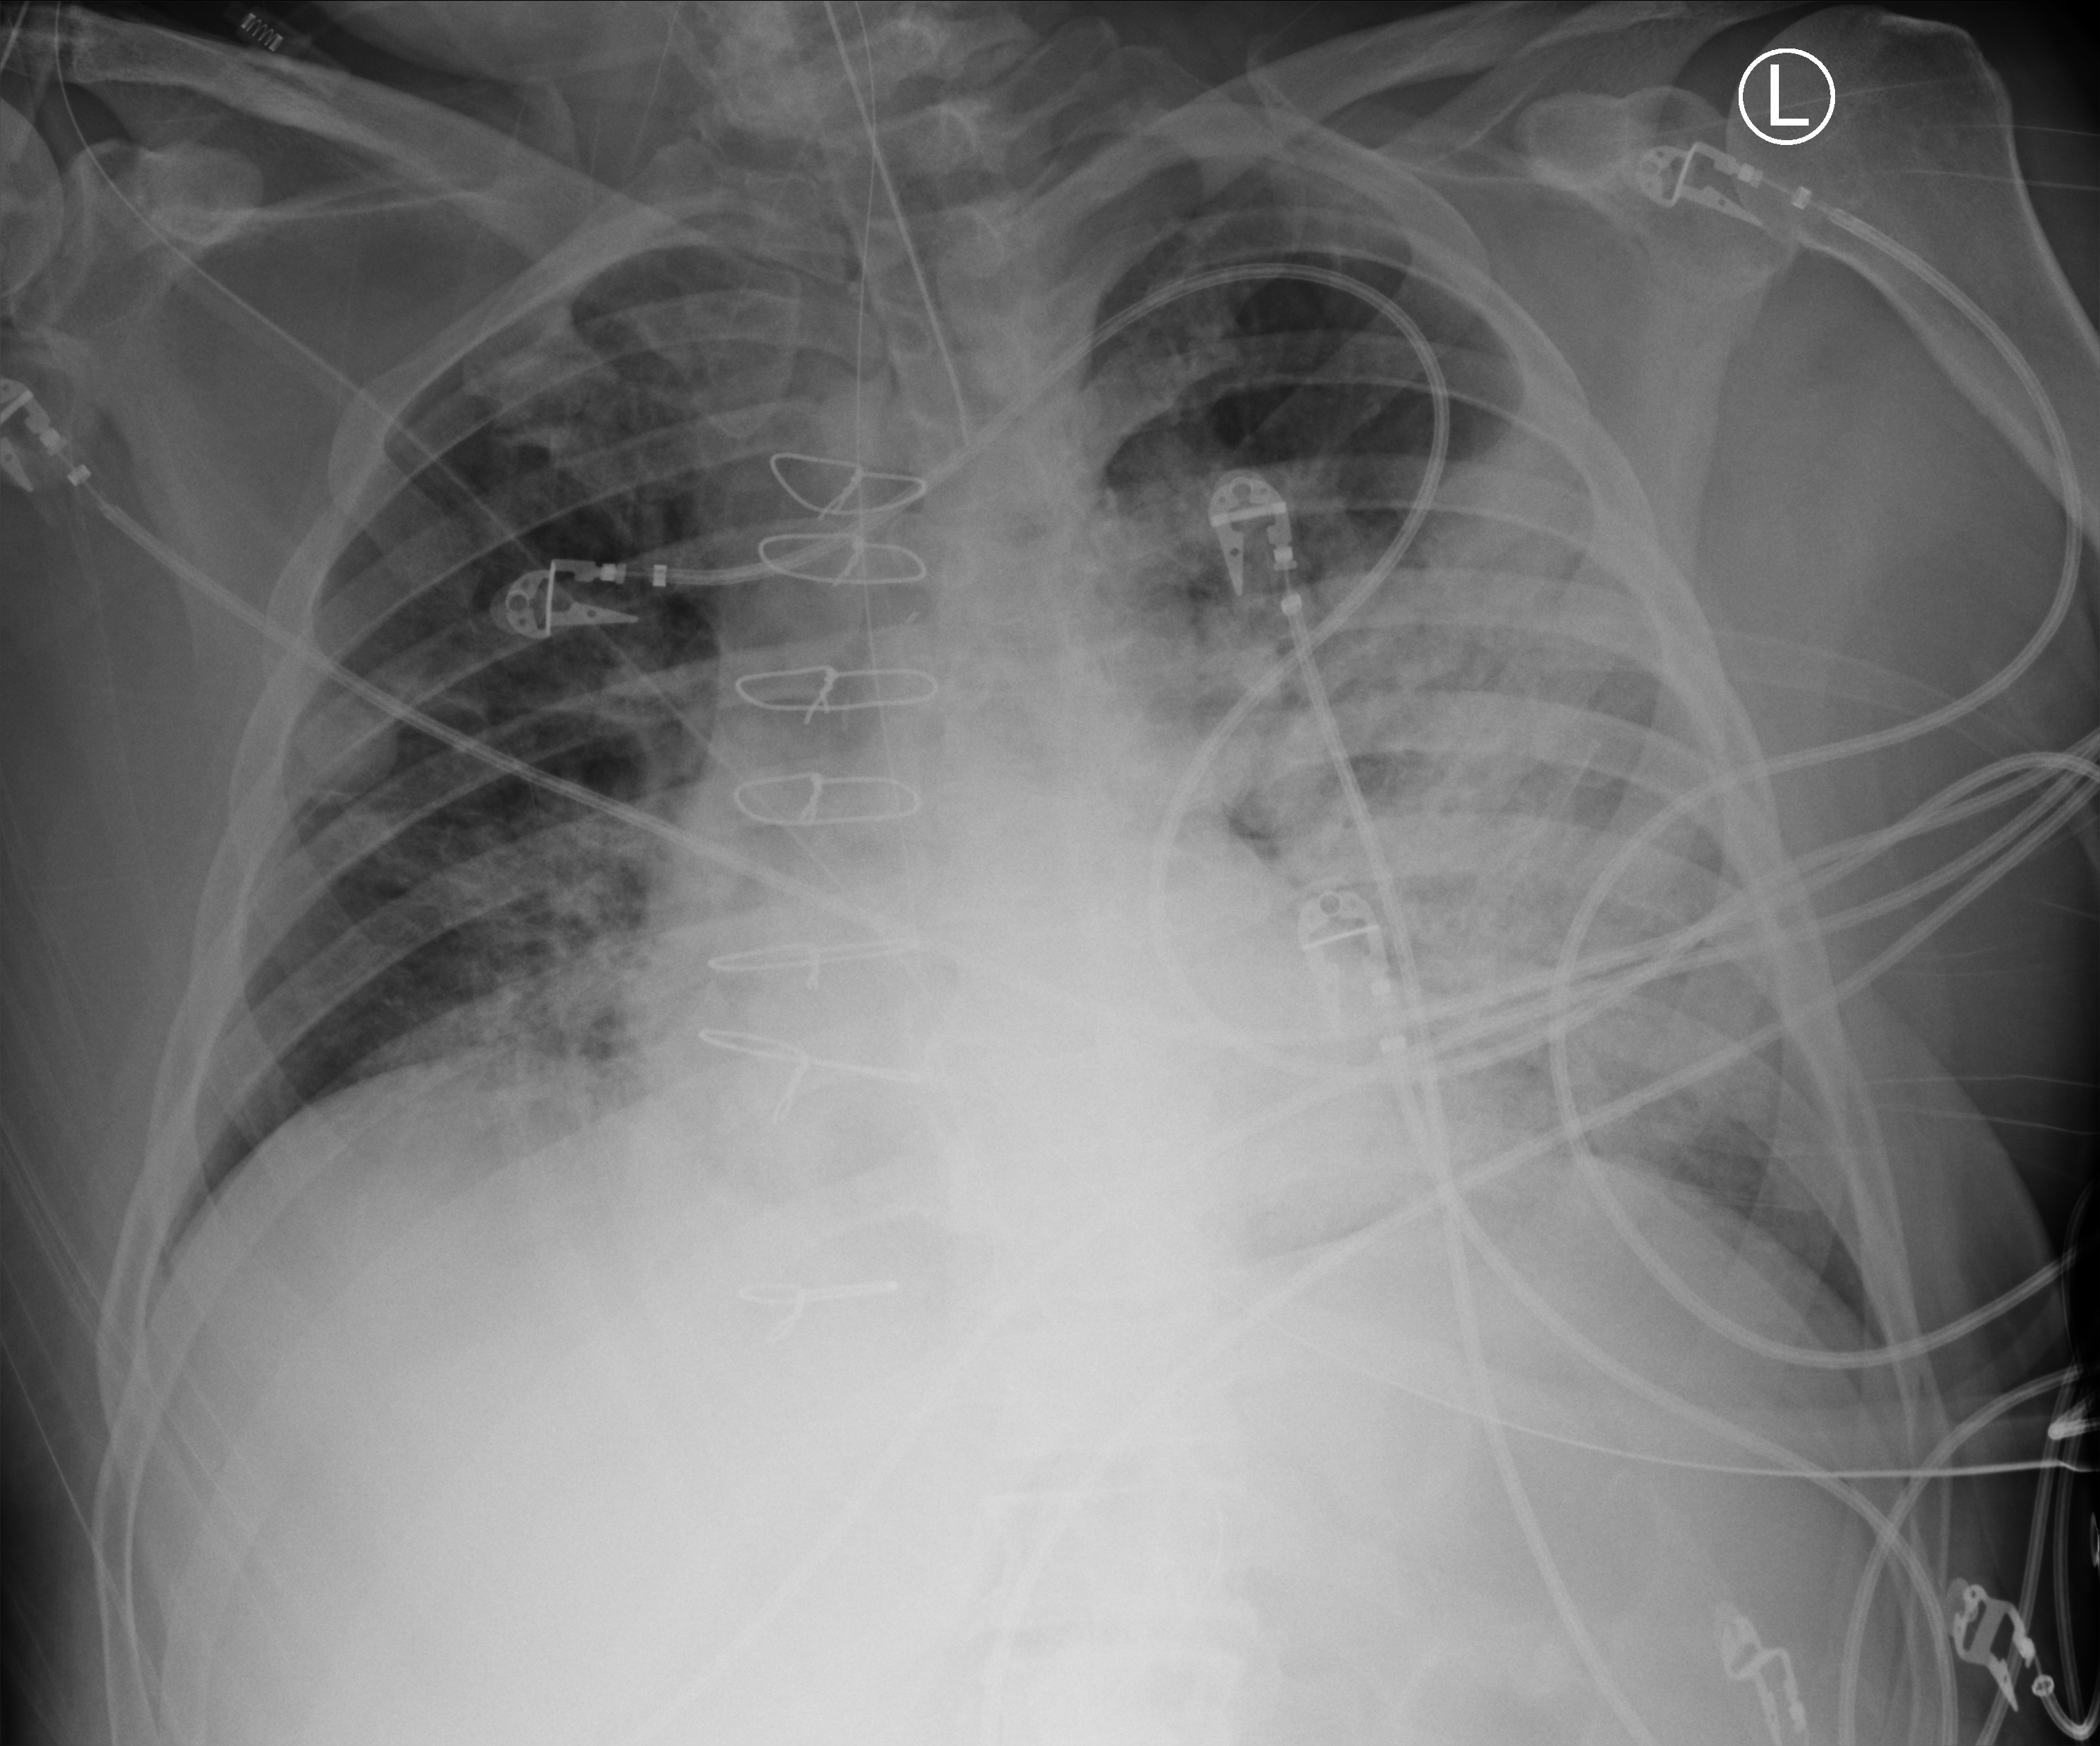
Portable chest radiograph, anteroposterior (AP) projection. Male patient hospitalised with COVID-19, age 60–74 years.
From the hospital-stay record, not from the radiograph (when in the stay this image was taken is not recorded):
- mechanically ventilated during this hospital stay: yes
- length of hospital stay: 44 days
- admitted to intensive care during this hospital stay: yes